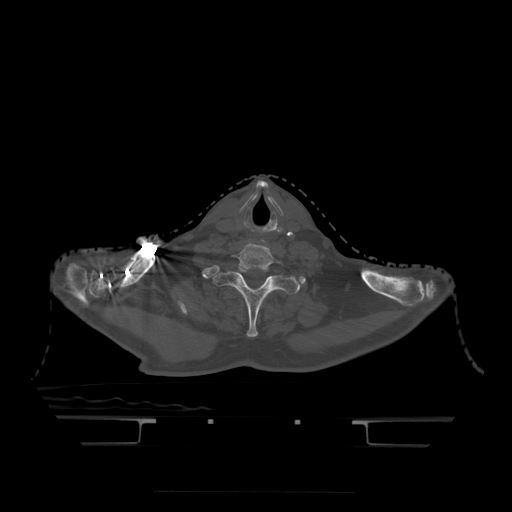
CT including the spine, one axial slice. Slice 403 of 522 in the series (ordered by position). Bone window (W 1800 / L 400 HU). 1.25 mm slice thickness. 512 × 512 image matrix, field of view 436 × 436 mm. Patient age 68 years. Case-level facts recorded for this patient, not image findings: primary cancer: urothelial.
Structures marked on this image (semi-automatically segmented with operator editing):
- T1 vertebra: bounding box <218,266,300,338> (left, top, right, bottom; pixels)